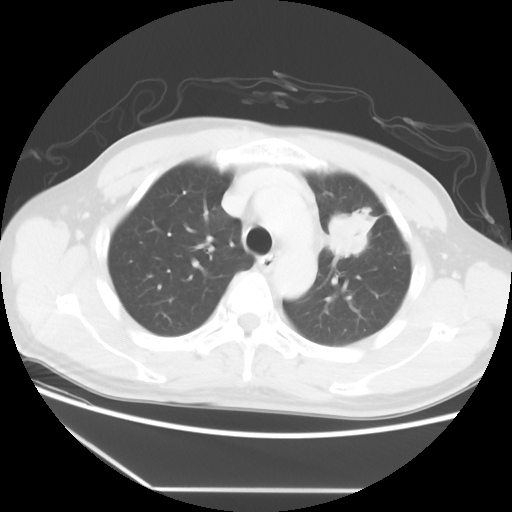
Chest CT, one axial slice; slice 41 of 56 in the series (ordered by position); 120 kVp; lung window (W 1500 / L -600 HU); 512 × 512 image matrix, field of view 373 × 373 mm. Patient: male, 53 years. From the clinical record (not read from this slice): clinical TNM (as recorded): T2a N1 M1b.
Annotated regions visible in this slice (bounding box drawn by a radiologist):
- lung tumour (recorded histology: adenocarcinoma): bounding box <327,203,378,262> (left, top, right, bottom; pixels)